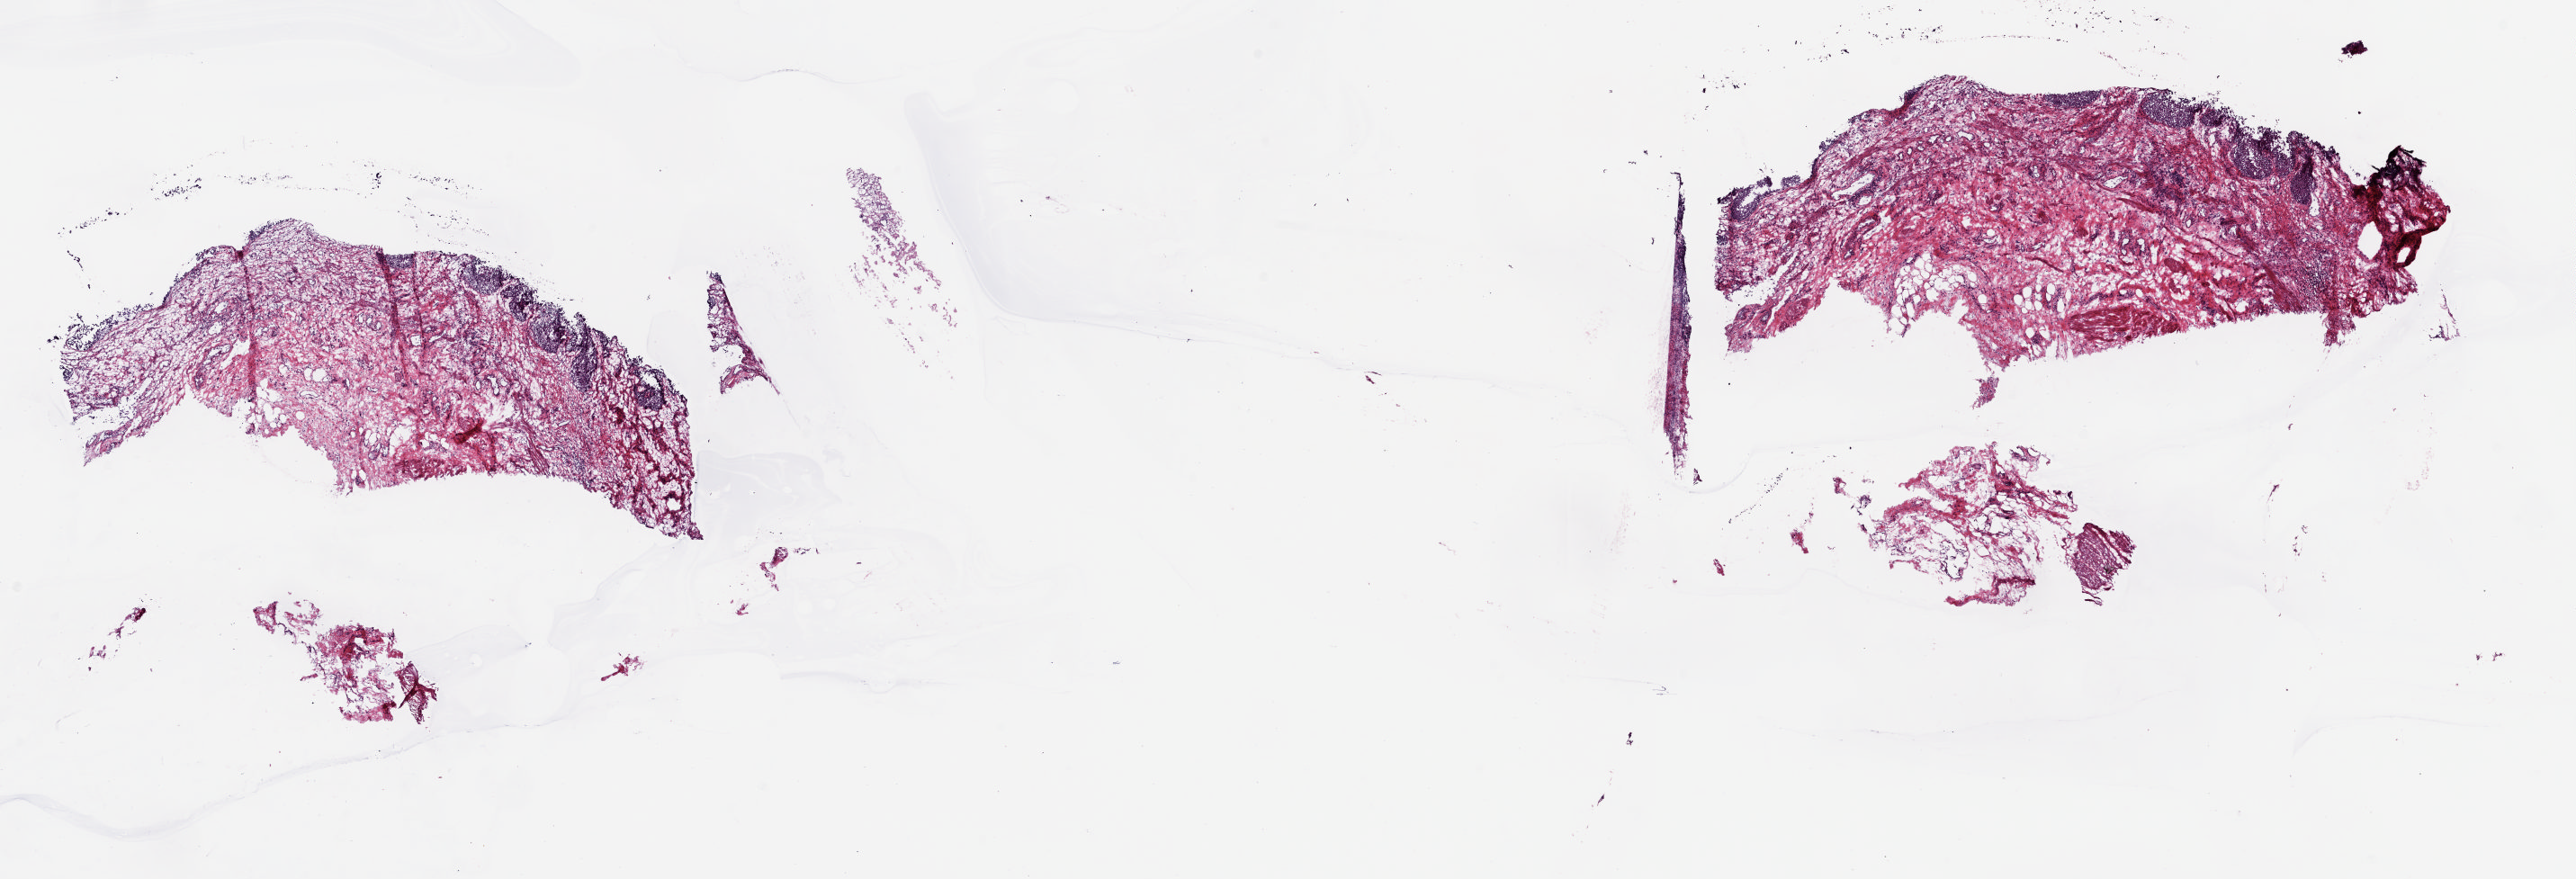
Whole-slide histology image, Hematoxylin and eosin (H&E) stained — shown as a low-resolution overview of the whole scanned area (about 22.7 x 7.8 mm, acquisition: 20x scan); frozen section from the top of the tissue portion; bladder, solid tissue normal (non-tumour tissue) sample. Female patient; age at initial diagnosis 59 years. Slide review estimates, as recorded: tumour cells 0%, tumour nuclei 0%, normal cells 20%, stromal cells 80%, necrosis 0%. Infiltration values recorded for this section: lymphocyte infiltration 0%, monocyte infiltration 0%, neutrophil infiltration 0%.
This section: solid tissue normal (non-tumour) sample from the same patient. Patient diagnosis: Transitional cell carcinoma (lateral wall of bladder).